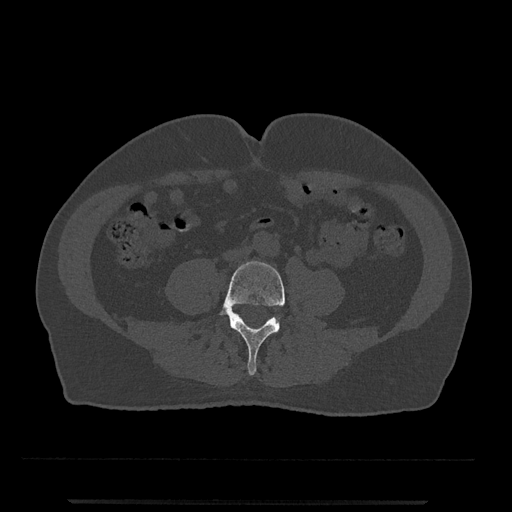
CT including the spine, one axial slice; position 132 of 797 along the scan axis; reconstruction kernel Br40s/3; 120 kVp; bone window (W 1800 / L 400 HU); 0.5 mm slice thickness; 512 × 512 image matrix, field of view 419 × 419 mm. Patient: male, 63 years. From the clinical record (not read from this slice): primary cancer: prostate.
Structures marked on this image (semi-automatically segmented with operator editing):
- L4 vertebra: bounding box <218,261,285,375> (left, top, right, bottom; pixels)